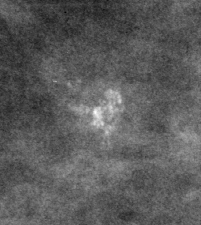
Crop from a digitized film mammogram around one marked abnormality, left breast, CC view.
- Calcifications, morphology pleomorphic, distribution clustered; BI-RADS assessment category 4; subtlety rating 4 on a 1 (subtle) to 5 (obvious) scale; pathology result (as recorded, not read from the image): benign.